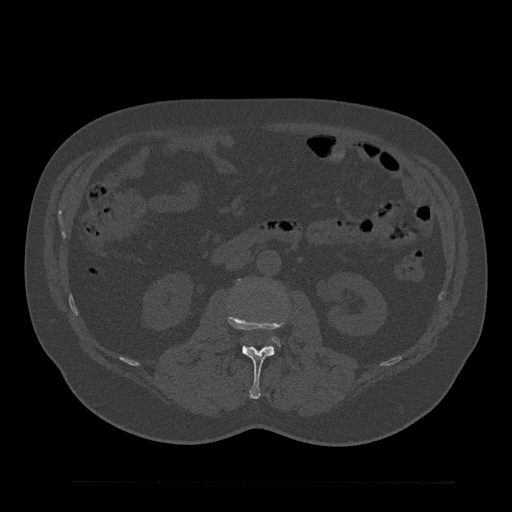
CT including the spine, one axial slice; position 79 of 797 along the scan axis; 120 kVp; bone window (W 1800 / L 400 HU); 0.5 mm slice thickness; 512 × 512 image matrix, field of view 430 × 430 mm. Patient: male, 61 years. From the clinical record (not read from this slice): primary cancer: prostate.
Outlined on this slice (semi-automatically segmented with operator editing):
- L2 vertebra: bounding box [x1, y1, x2, y2] px = [227, 312, 287, 399]
- L3 vertebra: [273, 338, 278, 343]